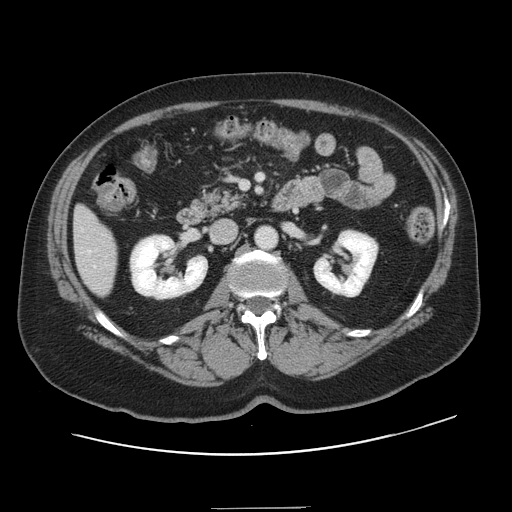
Contrast-enhanced abdominal CT, one axial slice; slice 55 of 143 in the series (ordered by position); intravenous contrast given; soft-tissue window (W 400 / L 40 HU); 2.5 mm slice thickness; 512 × 512 image matrix. Male patient, age 62 years. Case-level facts recorded for this patient, not image findings: diagnosis: colorectal cancer liver metastases, imaged before liver resection; multiple liver metastases: yes; largest metastasis: 2.7 cm; disease in both lobes: no.
Outlined on this slice (outlined manually by an expert reader):
- hepatic veins: bounding box [x1, y1, x2, y2] px = [89, 251, 95, 267]
- liver: [74, 208, 117, 296]